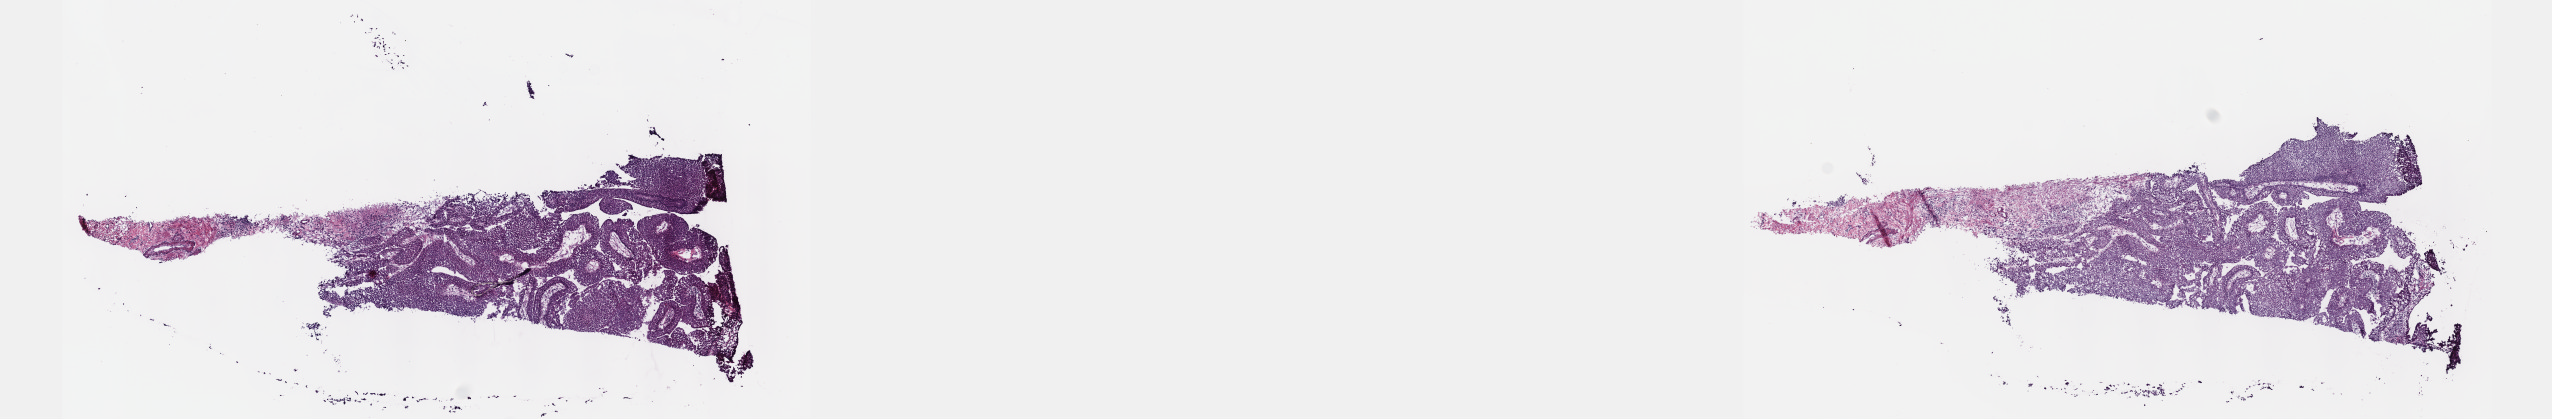
Whole-slide histology image, Hematoxylin and eosin (H&E) stained, a low-resolution overview of the entire scanned area, about 20.6 x 3.4 mm (slide scanned at 40x); frozen section; bladder, primary tumour sample. Female patient; age at initial diagnosis 69 years. Histologic grade: high grade. Slide review estimates, as recorded: tumour cells 80%, tumour nuclei 90%, normal cells 20%, stromal cells 0%, necrosis 0%. Infiltration values recorded for this section: lymphocyte infiltration 0%, monocyte infiltration 0%, neutrophil infiltration 0%.
Lymph nodes positive (case pathology): 0 of 38 examined. AJCC pathologic stage: II (7th edition). Histologic diagnosis: Papillary transitional cell carcinoma.